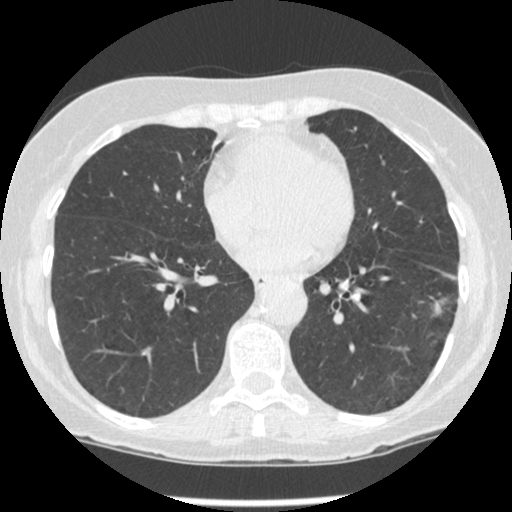
Low-dose screening chest CT, one axial slice; position 101 of 247 along the scan axis; reconstruction kernel STANDARD; lung window (W 1500 / L -600 HU); 512 × 512 image matrix.
Annotated regions visible in this slice (manually delineated by an expert):
- lesion 1 (tumor, lower lobe of left lung): bounding box (x1, y1, x2, y2) in pixels: (434, 299, 445, 315)